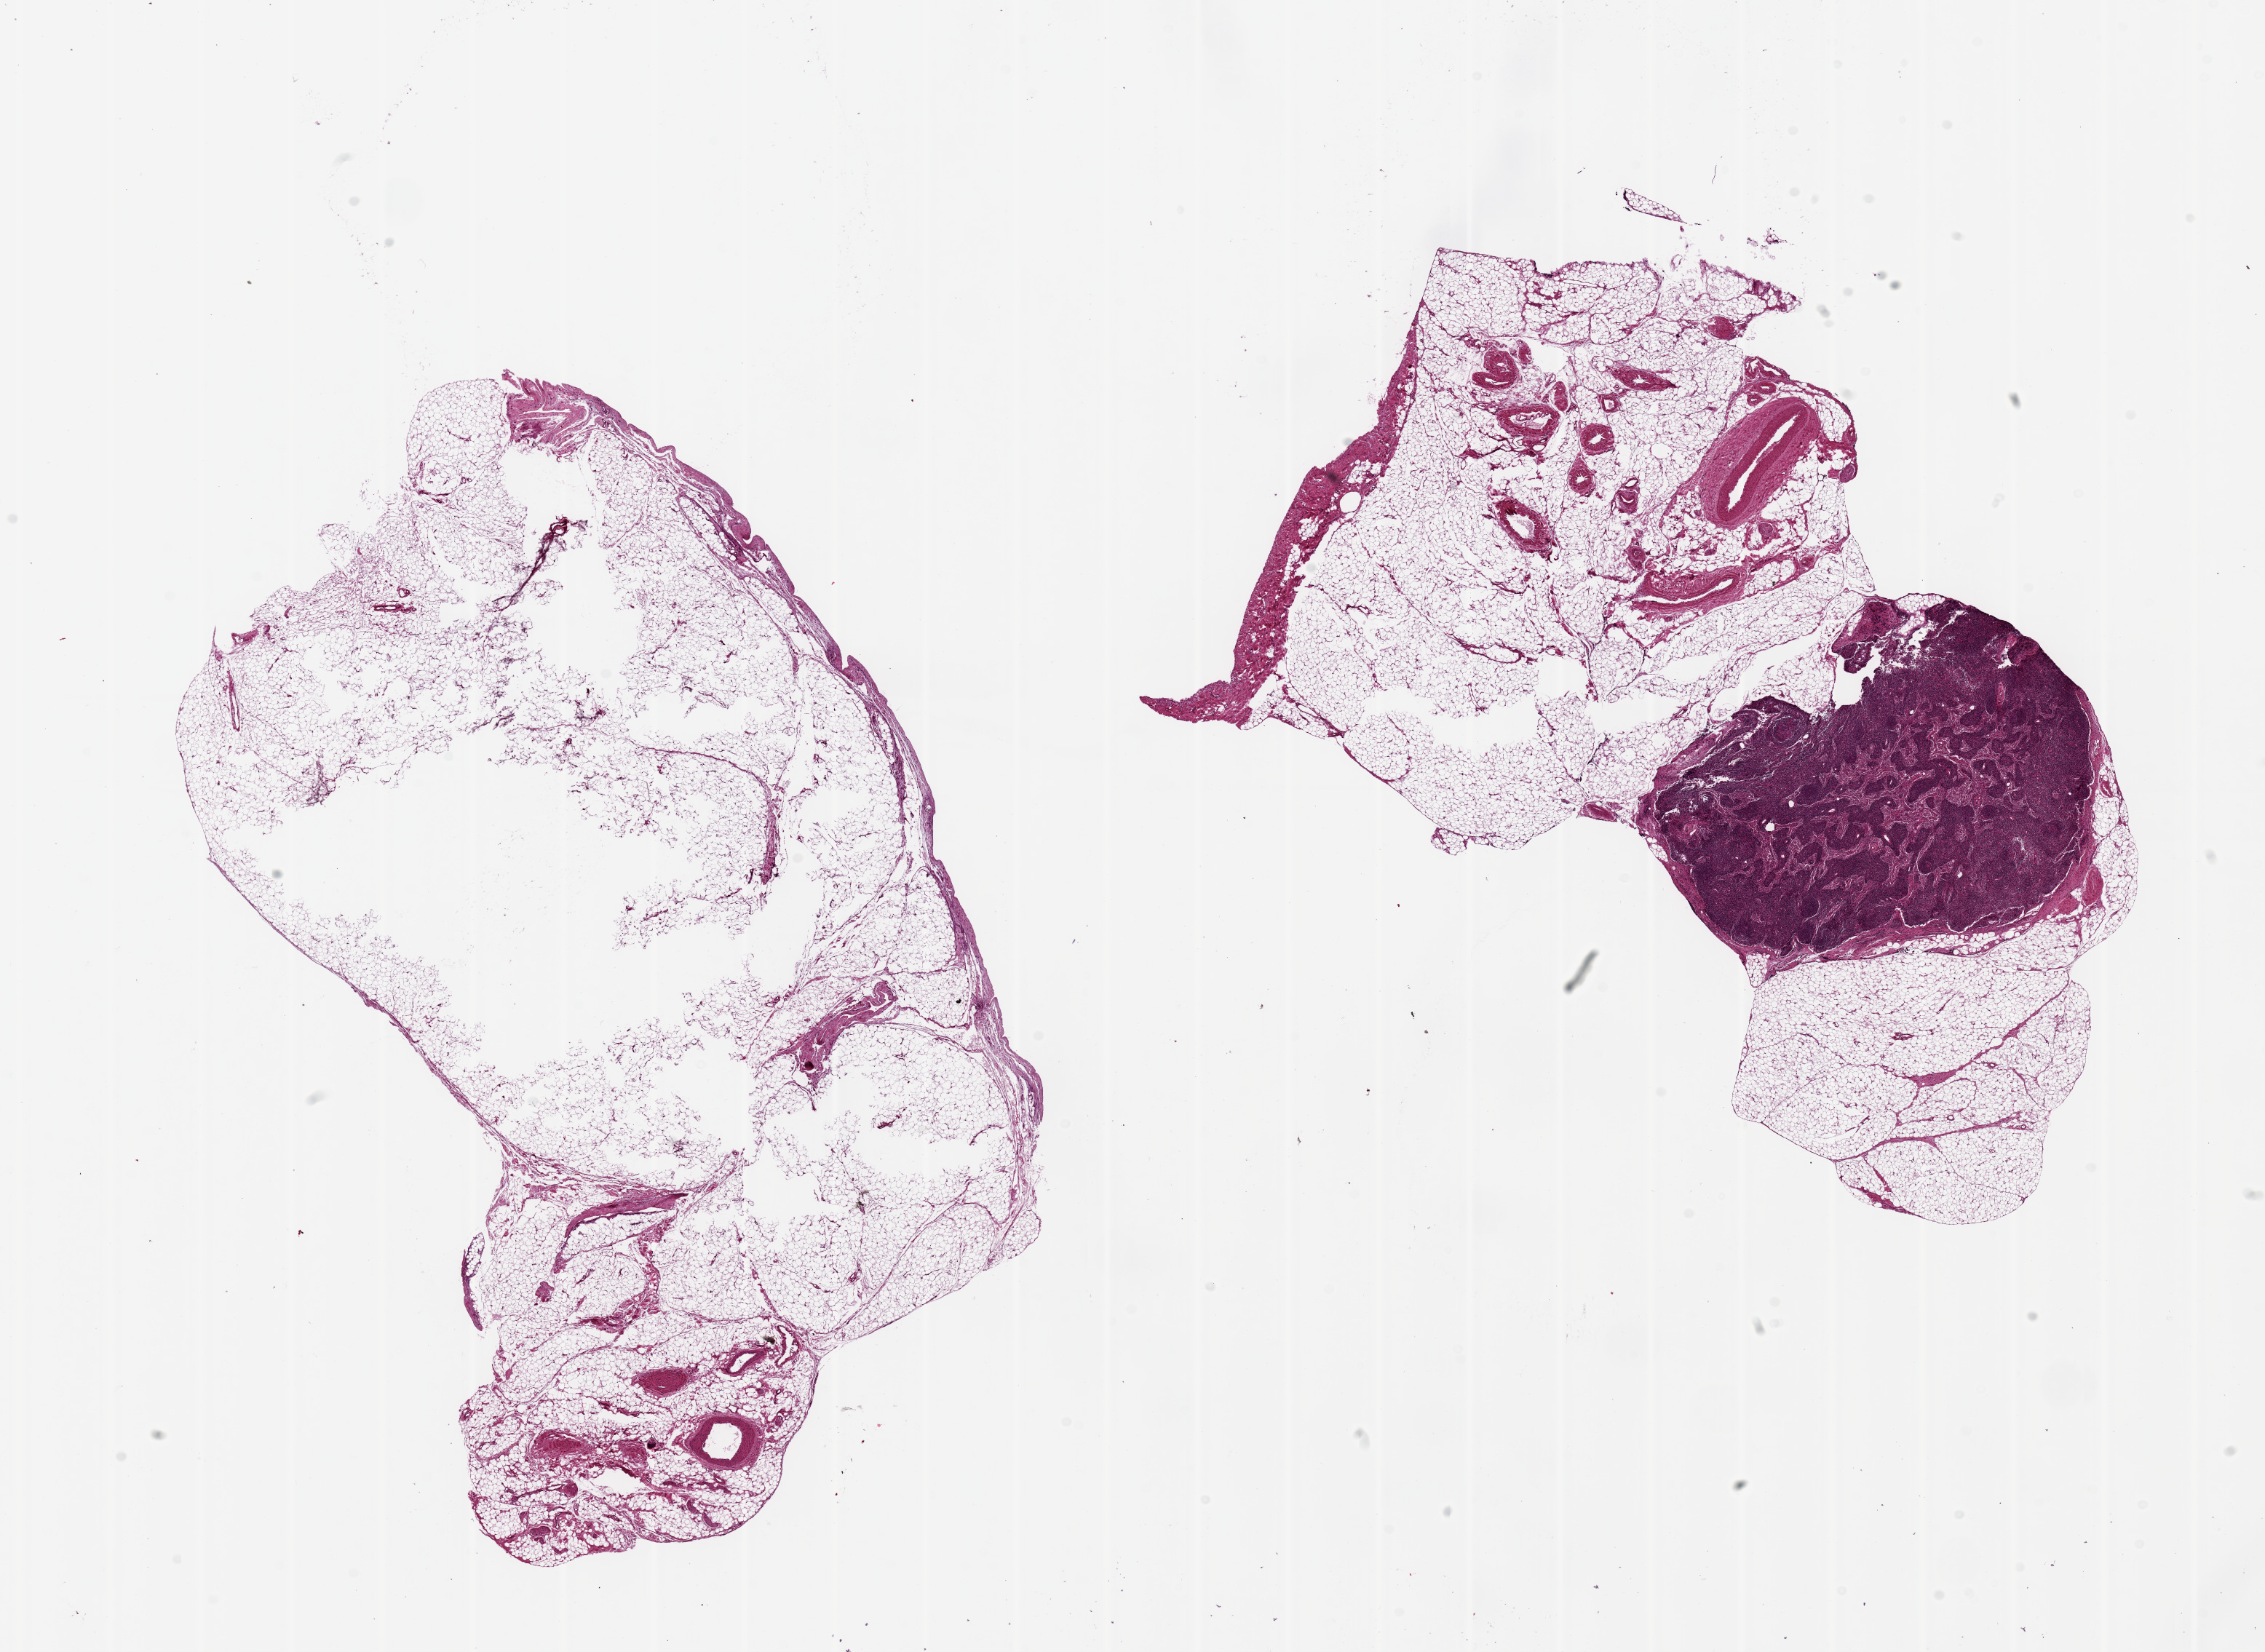
Whole-slide image, hematoxylin and eosin (H&E) stain, a low-resolution overview of the entire scanned area, about 24.6 x 18.0 mm (from a 20x scan), PAXgene-fixed paraffin-embedded (PFPE) section, section of omentum (target tissue), tissue donor sample. Female donor.
Reviewer comment on this tissue sample: 2 pieces, 13x8 & 12x8mm; 1 piece has a 5x4mm lymph node; other has a central 4mm fixation defect.